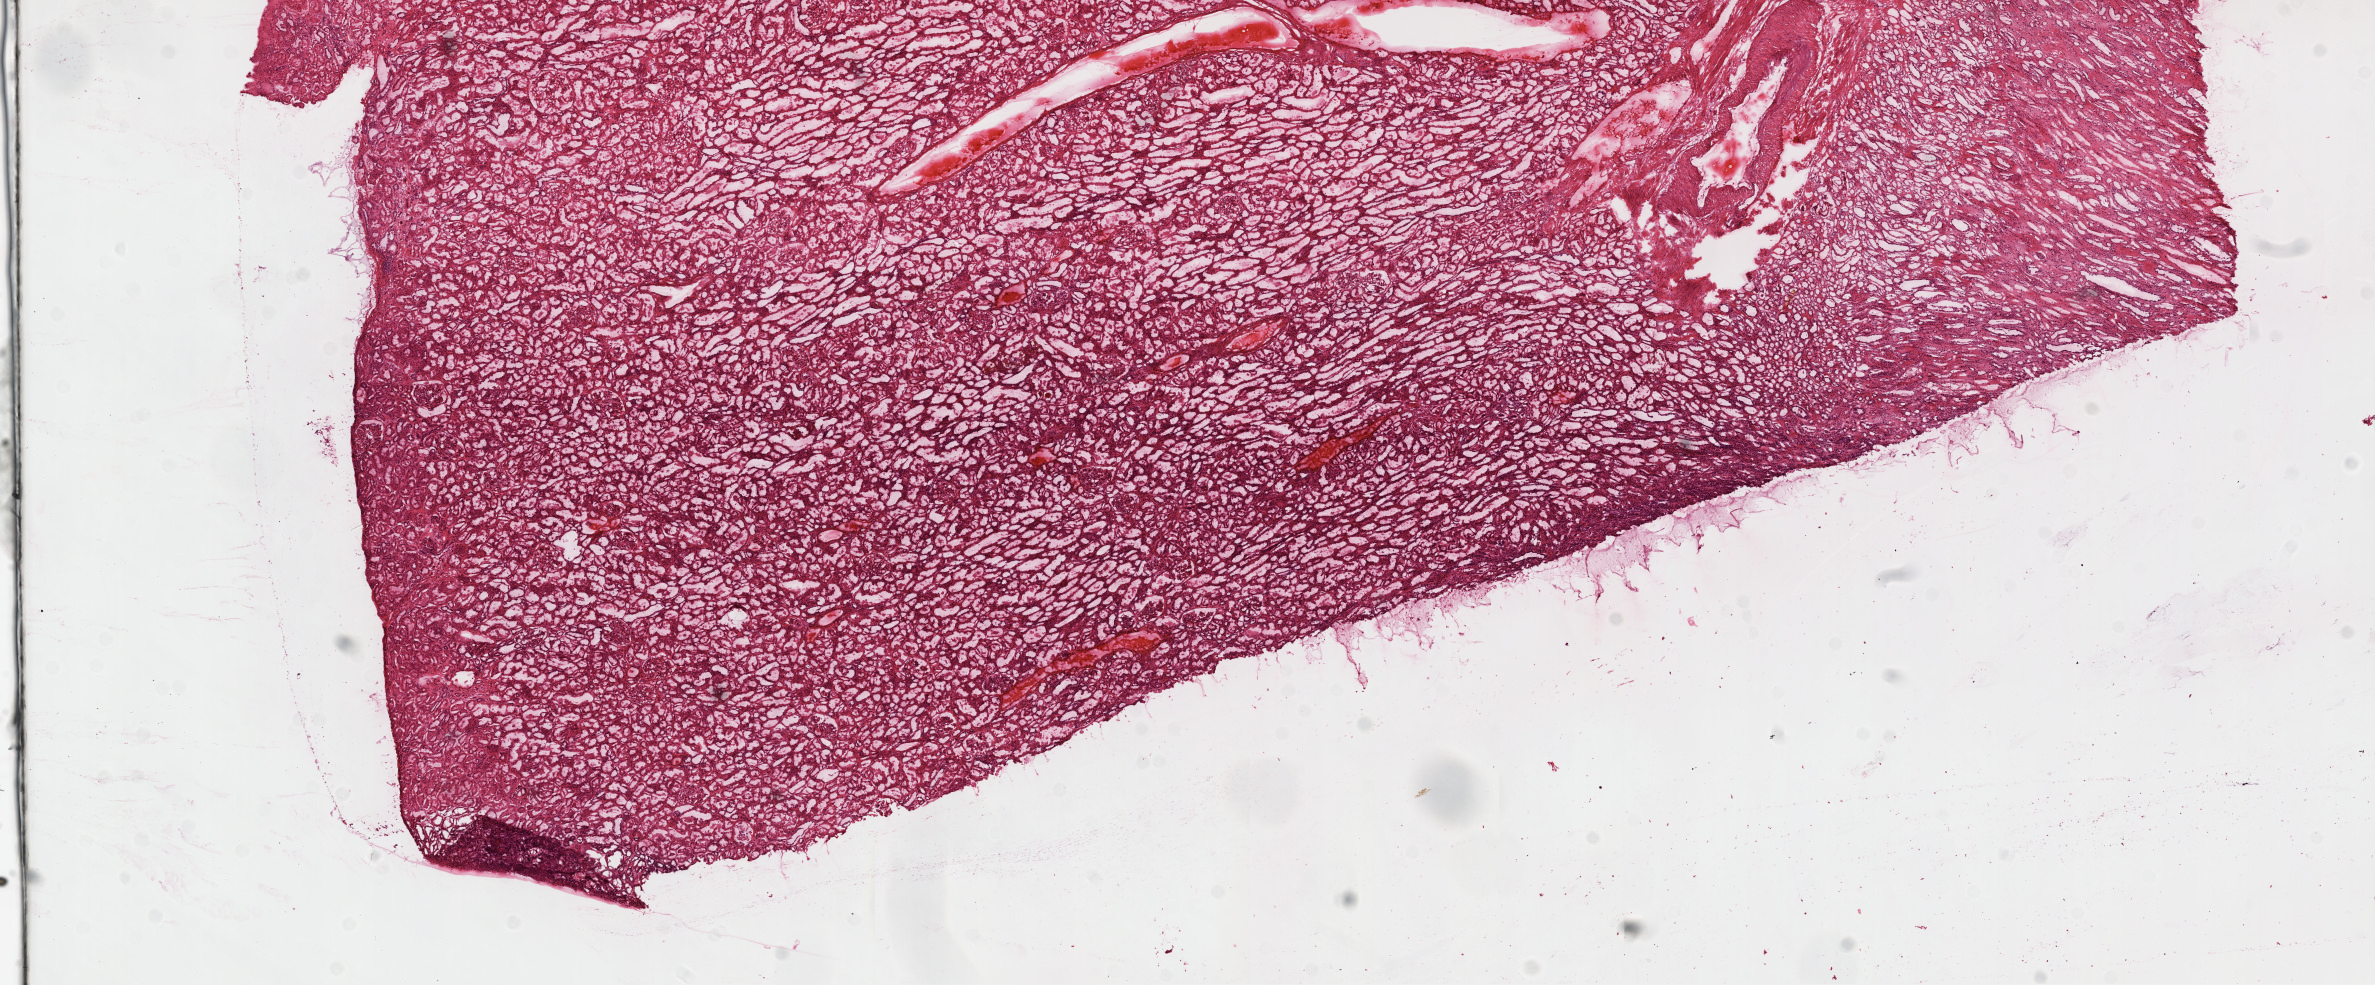
Digitized H&E-stained tissue section (whole slide) — shown as a low-resolution overview of the whole scanned area (about 19.1 x 7.9 mm, from a 20x scan). Frozen section from the top of the tissue portion. Solid tissue normal (non-tumour tissue) sample from the kidney. Male, age 78 years at initial diagnosis.
This section: solid tissue normal (non-tumour) sample from the same patient. Patient diagnosis: Clear cell adenocarcinoma, NOS.